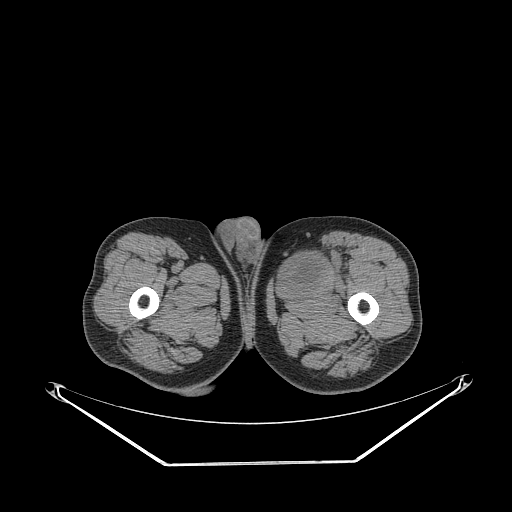
CT of an extremity soft-tissue mass (from a PET/CT study), one axial slice; position 263 of 267 along the scan axis; 140 kVp; soft-tissue window (W 400 / L 40 HU); 3.75 mm slice thickness; 512 × 512 image matrix, field of view 500 × 500 mm. Male patient. Case-level facts recorded for this patient, not image findings: histological type: pleiomorphic liposarcoma; grade: high; site of the primary tumour: left thigh.
Structures marked on this image (expert contour drawn on MRI and transferred to this co-registered scan by the dataset authors):
- gross tumour volume including surrounding oedema: box from (x=281, y=244) to (x=346, y=293) px
- gross tumour volume (mass): (x=281, y=251)–(x=328, y=287)